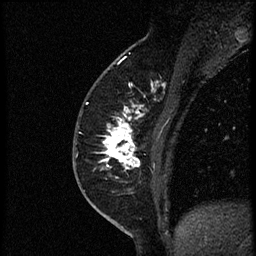
Breast MRI (dynamic contrast-enhanced), one sagittal slice. Position 24 of 56 along the scan axis. Dynamic contrast-enhanced study with each time point stored as its own series, time point 2 of 4 at this slice position (early post-contrast, ordered by acquisition time). 1.5 T. TE 4.2 ms, TR 18.9 ms. 2 mm slice thickness. 256 × 256 image matrix, field of view 200 × 200 mm. Female patient. Case-level facts recorded for this patient, not image findings: setting: breast cancer imaged before/during neoadjuvant chemotherapy; receptor status: HER2-positive.
Annotated regions visible in this slice (semi-automatic segmentation, software-assisted and operator-edited):
- analysis volume of interest (the breast-tissue region the enhancement analysis was run in; not a lesion): bounding box <94,86,173,189> (left, top, right, bottom; pixels)
- tumour enhancement mask (voxels above the 100 % enhancement threshold inside the analysis volume of interest): <100,104,143,170>